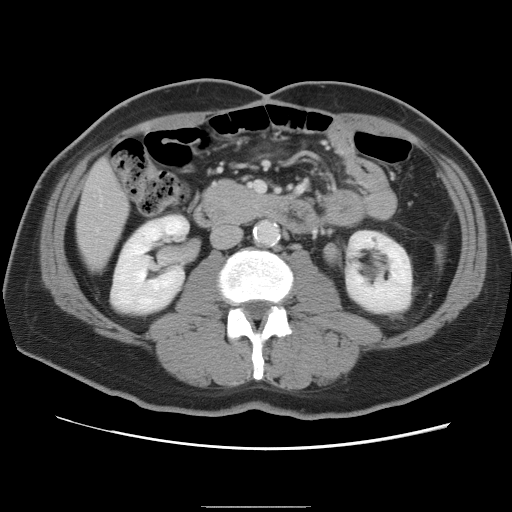
Contrast-enhanced abdominal CT, one axial slice. Slice 23 of 87 in the series (ordered by position). Intravenous contrast given. Soft-tissue window (W 400 / L 40 HU). 512 × 512 image matrix, field of view 363 × 363 mm. Male patient, age 63 years. From the clinical record (not read from this slice): diagnosis: colorectal cancer liver metastases, imaged before liver resection.
Outlined on this slice (expert manual segmentation):
- liver: bounding box (x1, y1, x2, y2) in pixels: (77, 162, 129, 270)
- planned liver remnant (the part of the liver to remain after resection): (77, 162, 129, 270)